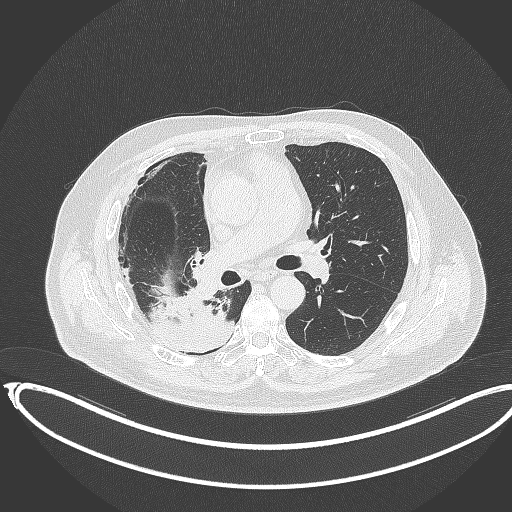
Chest CT, one axial slice. Slice 200 of 403 in the series (ordered by position). Reconstruction kernel B70f. 120 kVp. Lung window (W 1500 / L -600 HU). 1 mm slice thickness. 512 × 512 image matrix. Patient: male, 68 years. Case-level facts recorded for this patient, not image findings: clinical TNM (as recorded): T2a N0 M0.
Outlined on this slice (rectangle marked by the reading radiologist):
- lung tumour (recorded histology: adenocarcinoma): bounding box <144,289,237,352> (left, top, right, bottom; pixels)